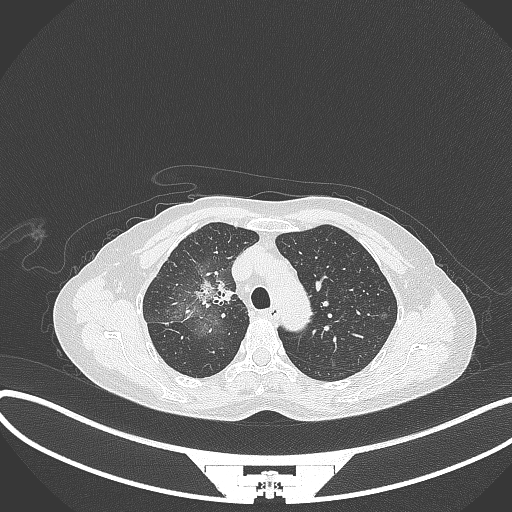
Chest CT, one axial slice; slice 231 of 284 in the series (ordered by position); reconstruction kernel B70f; 120 kVp; lung window (W 1500 / L -600 HU); 1 mm slice thickness; 512 × 512 image matrix. Patient: female, 59 years. From the clinical record (not read from this slice): clinical TNM (as recorded): T3 N0 M0.
Annotated regions visible in this slice (bounding box drawn by a radiologist):
- lung tumour (recorded histology: adenocarcinoma): bounding box [x1, y1, x2, y2] px = [196, 275, 233, 310]